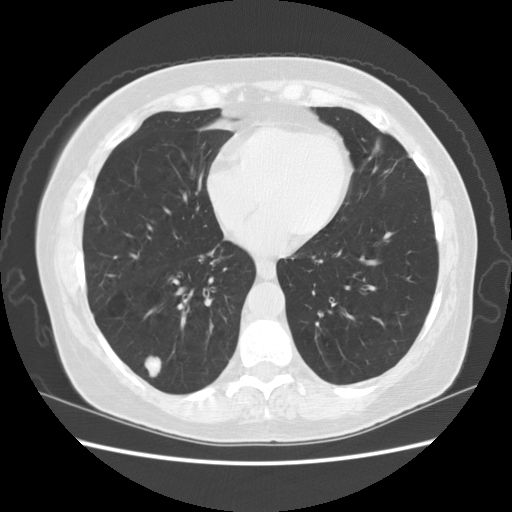
Low-dose screening chest CT, one axial slice; slice 51 of 156 in the series (ordered by position); reconstruction kernel STANDARD; lung window (W 1500 / L -600 HU); 512 × 512 image matrix, field of view 360 × 360 mm.
Structures marked on this image (manually delineated by an expert):
- lesion 1 (tumor, lower lobe of right lung): bounding box <145,357,161,377> (left, top, right, bottom; pixels)